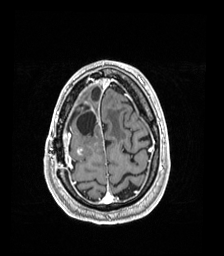
Brain MRI from a brain-tumour surgery series, one axial slice; position 37 of 192 along the scan axis; T1-weighted post-contrast; 224 × 256 image matrix, field of view 224 × 256 mm. From the clinical record (not read from this slice): histopathology: Astrocytoma; WHO grade: 4; IDH mutation: yes.
Outlined on this slice (outlined manually by an expert reader):
- previous resection cavity: bounding box <77,106,96,135> (left, top, right, bottom; pixels)
- tumour: <76,145,85,156>